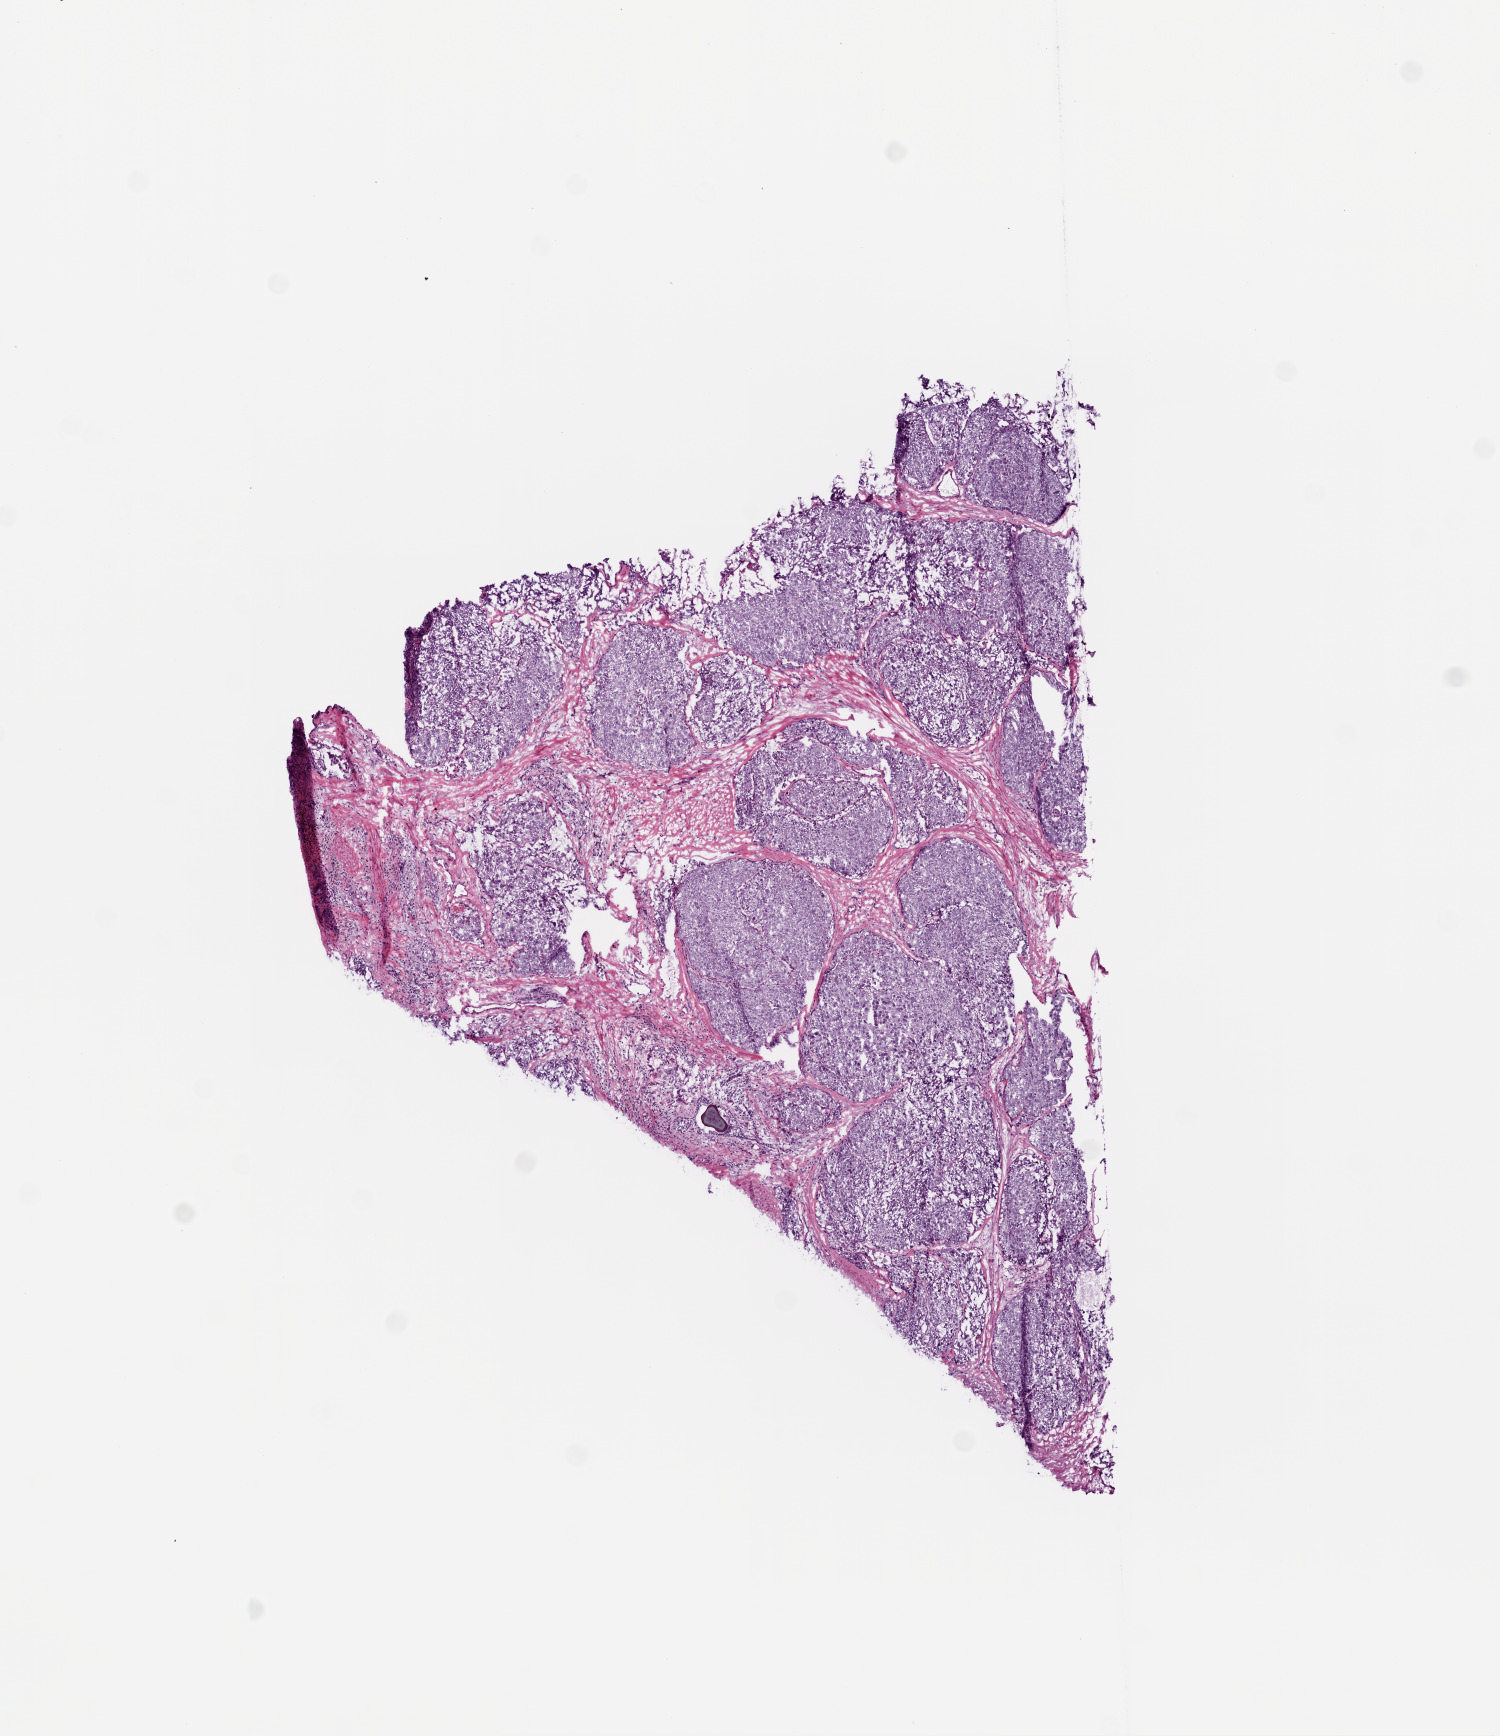
Whole-slide histology image, H&E-stained, whole scanned area (about 6.0 x 7.0 mm, acquisition: 20x scan) shown as a low-resolution overview; frozen section from the bottom of the tissue portion; primary tumour sample from the prostate. Patient: male, age at initial diagnosis 61 years. Gleason score: 9 (5+4). Slide review estimates, as recorded: tumour cells 70%, tumour nuclei 80%, normal cells 2%, stromal cells 25%, necrosis 3%. Infiltration values recorded for this section: lymphocyte infiltration 5%, monocyte infiltration 3%, neutrophil infiltration 0%.
* diagnosis: Acinar cell carcinoma (prostate gland)
* lymph nodes positive (case pathology): 0 of 5 examined